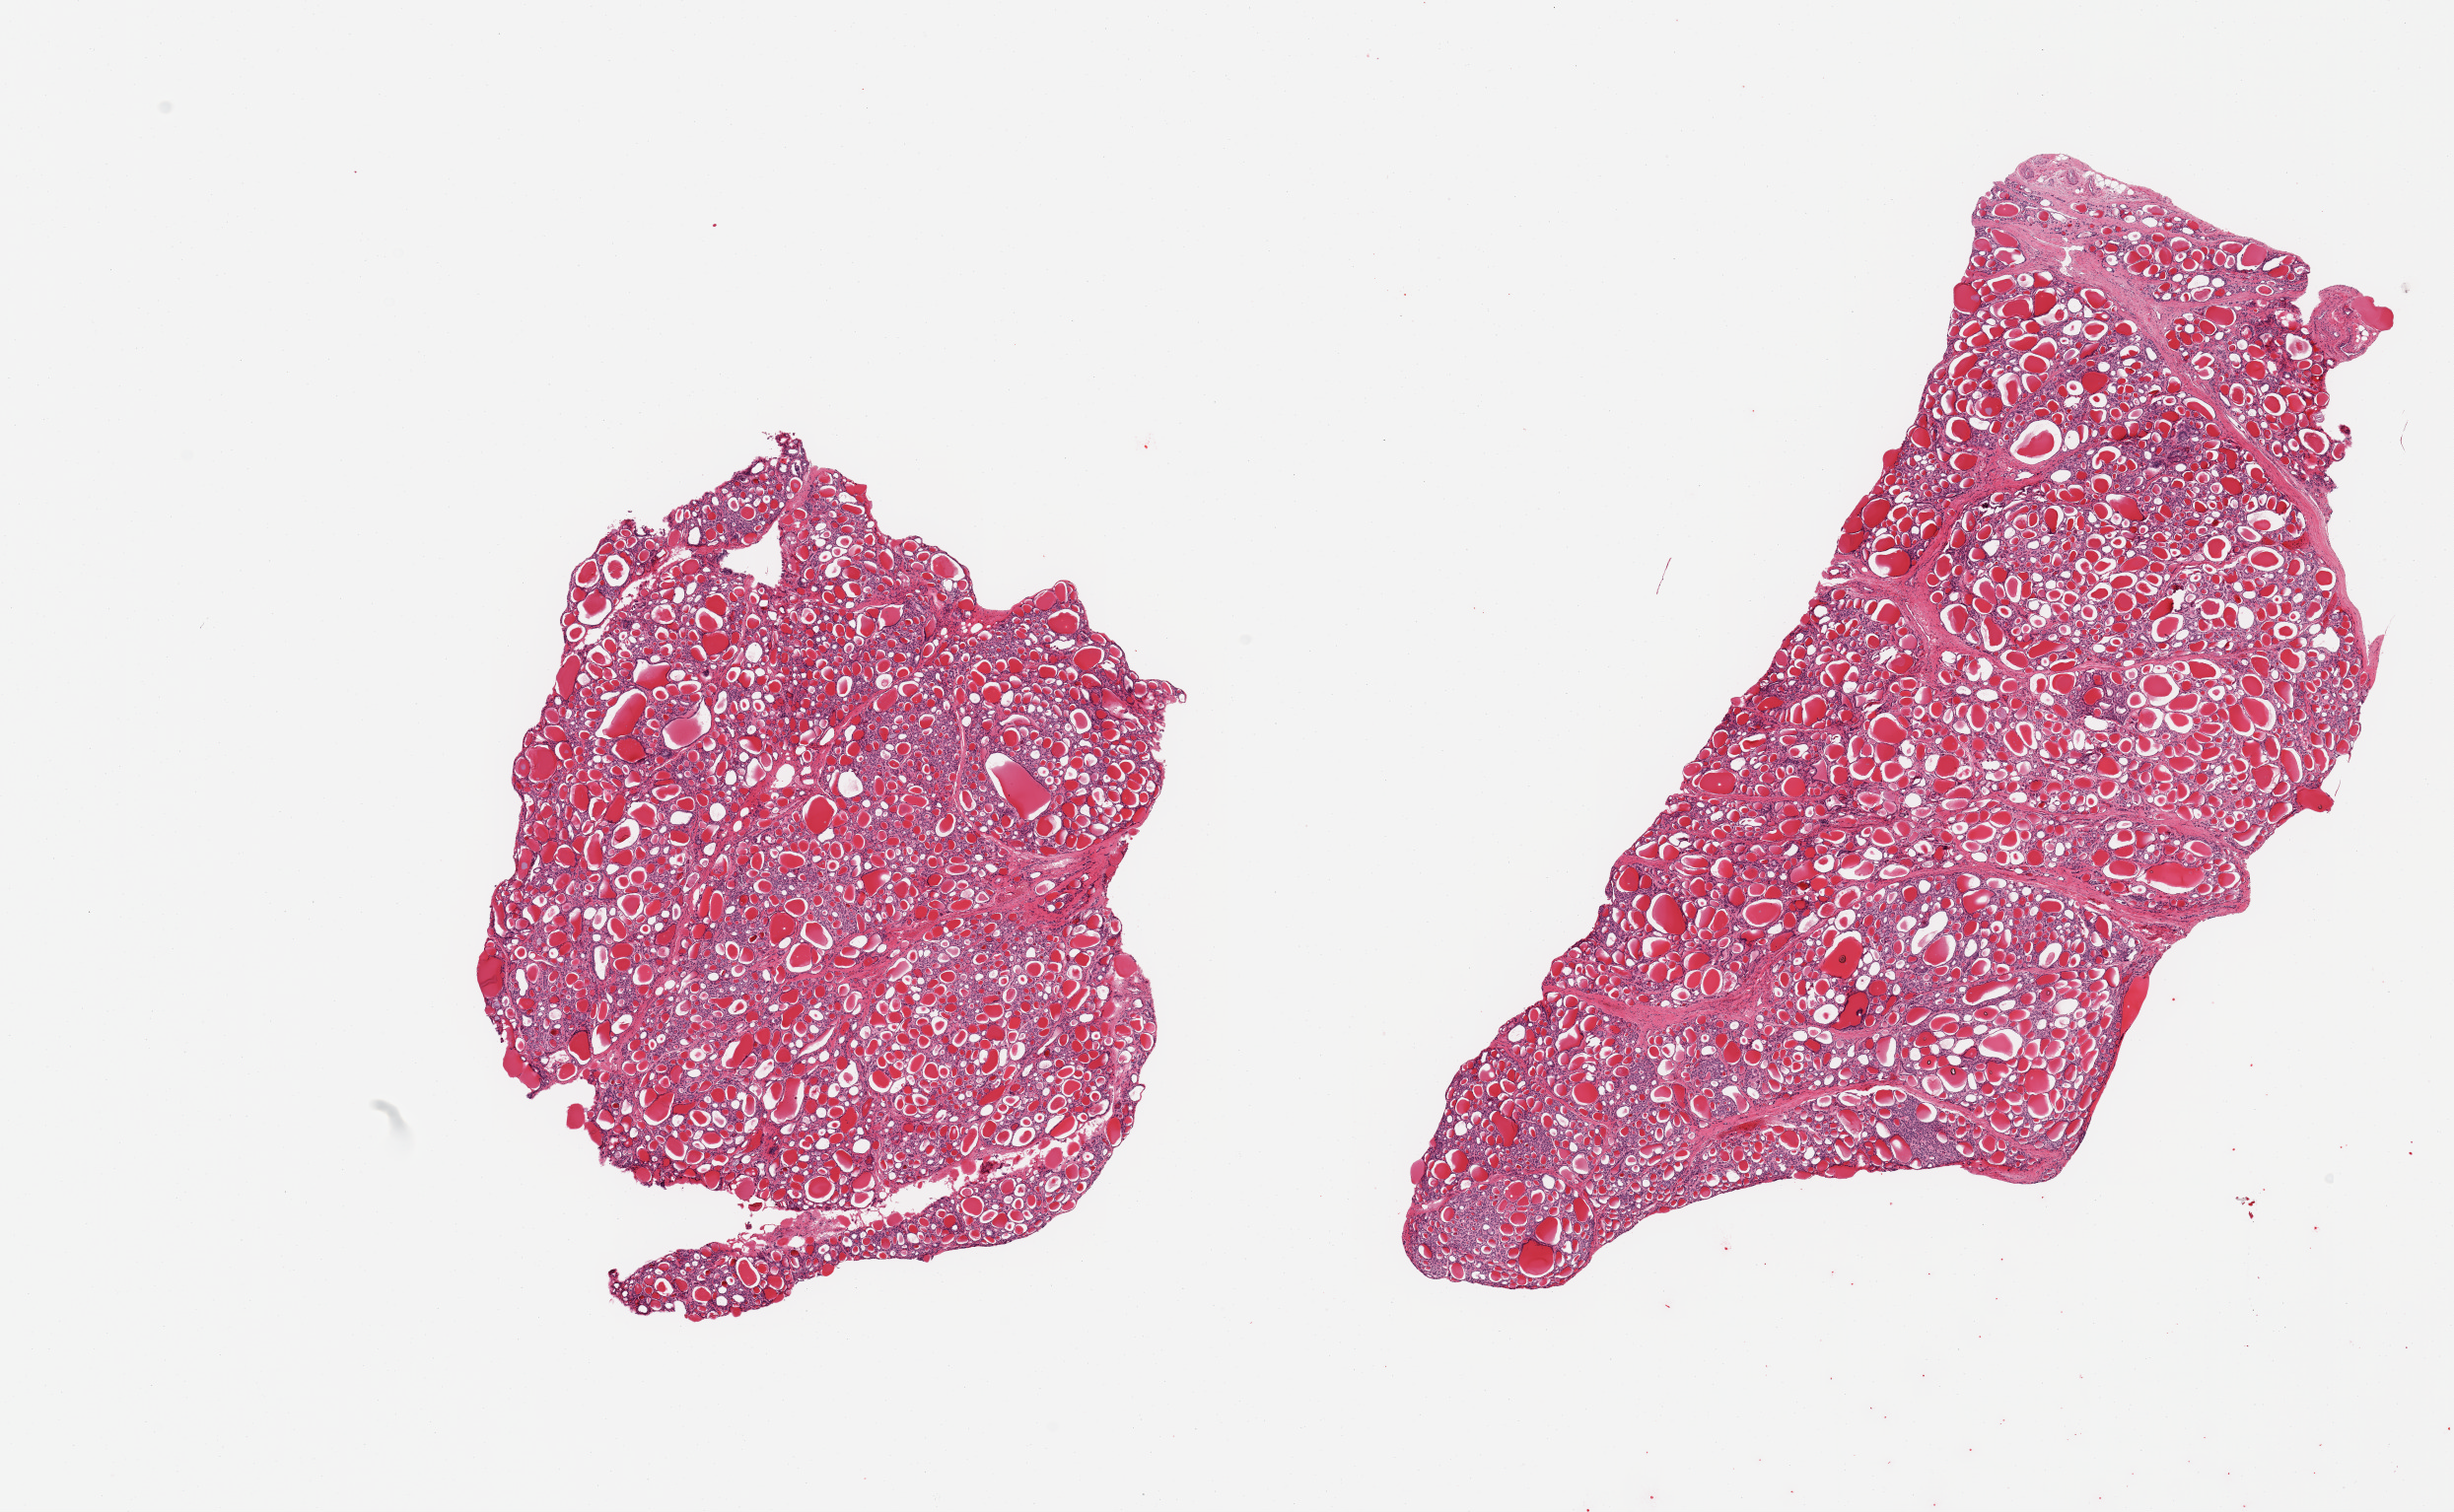
Digitized haematoxylin and eosin-stained section — low-resolution overview of the scanned area, about 19.7 x 12.1 mm. PAXgene-fixed, paraffin-embedded tissue. Sampled site (target tissue): thyroid. Donor tissue sample. Male donor.
Pathologist's review note for this sample: 2 pieces, no abnormalities.